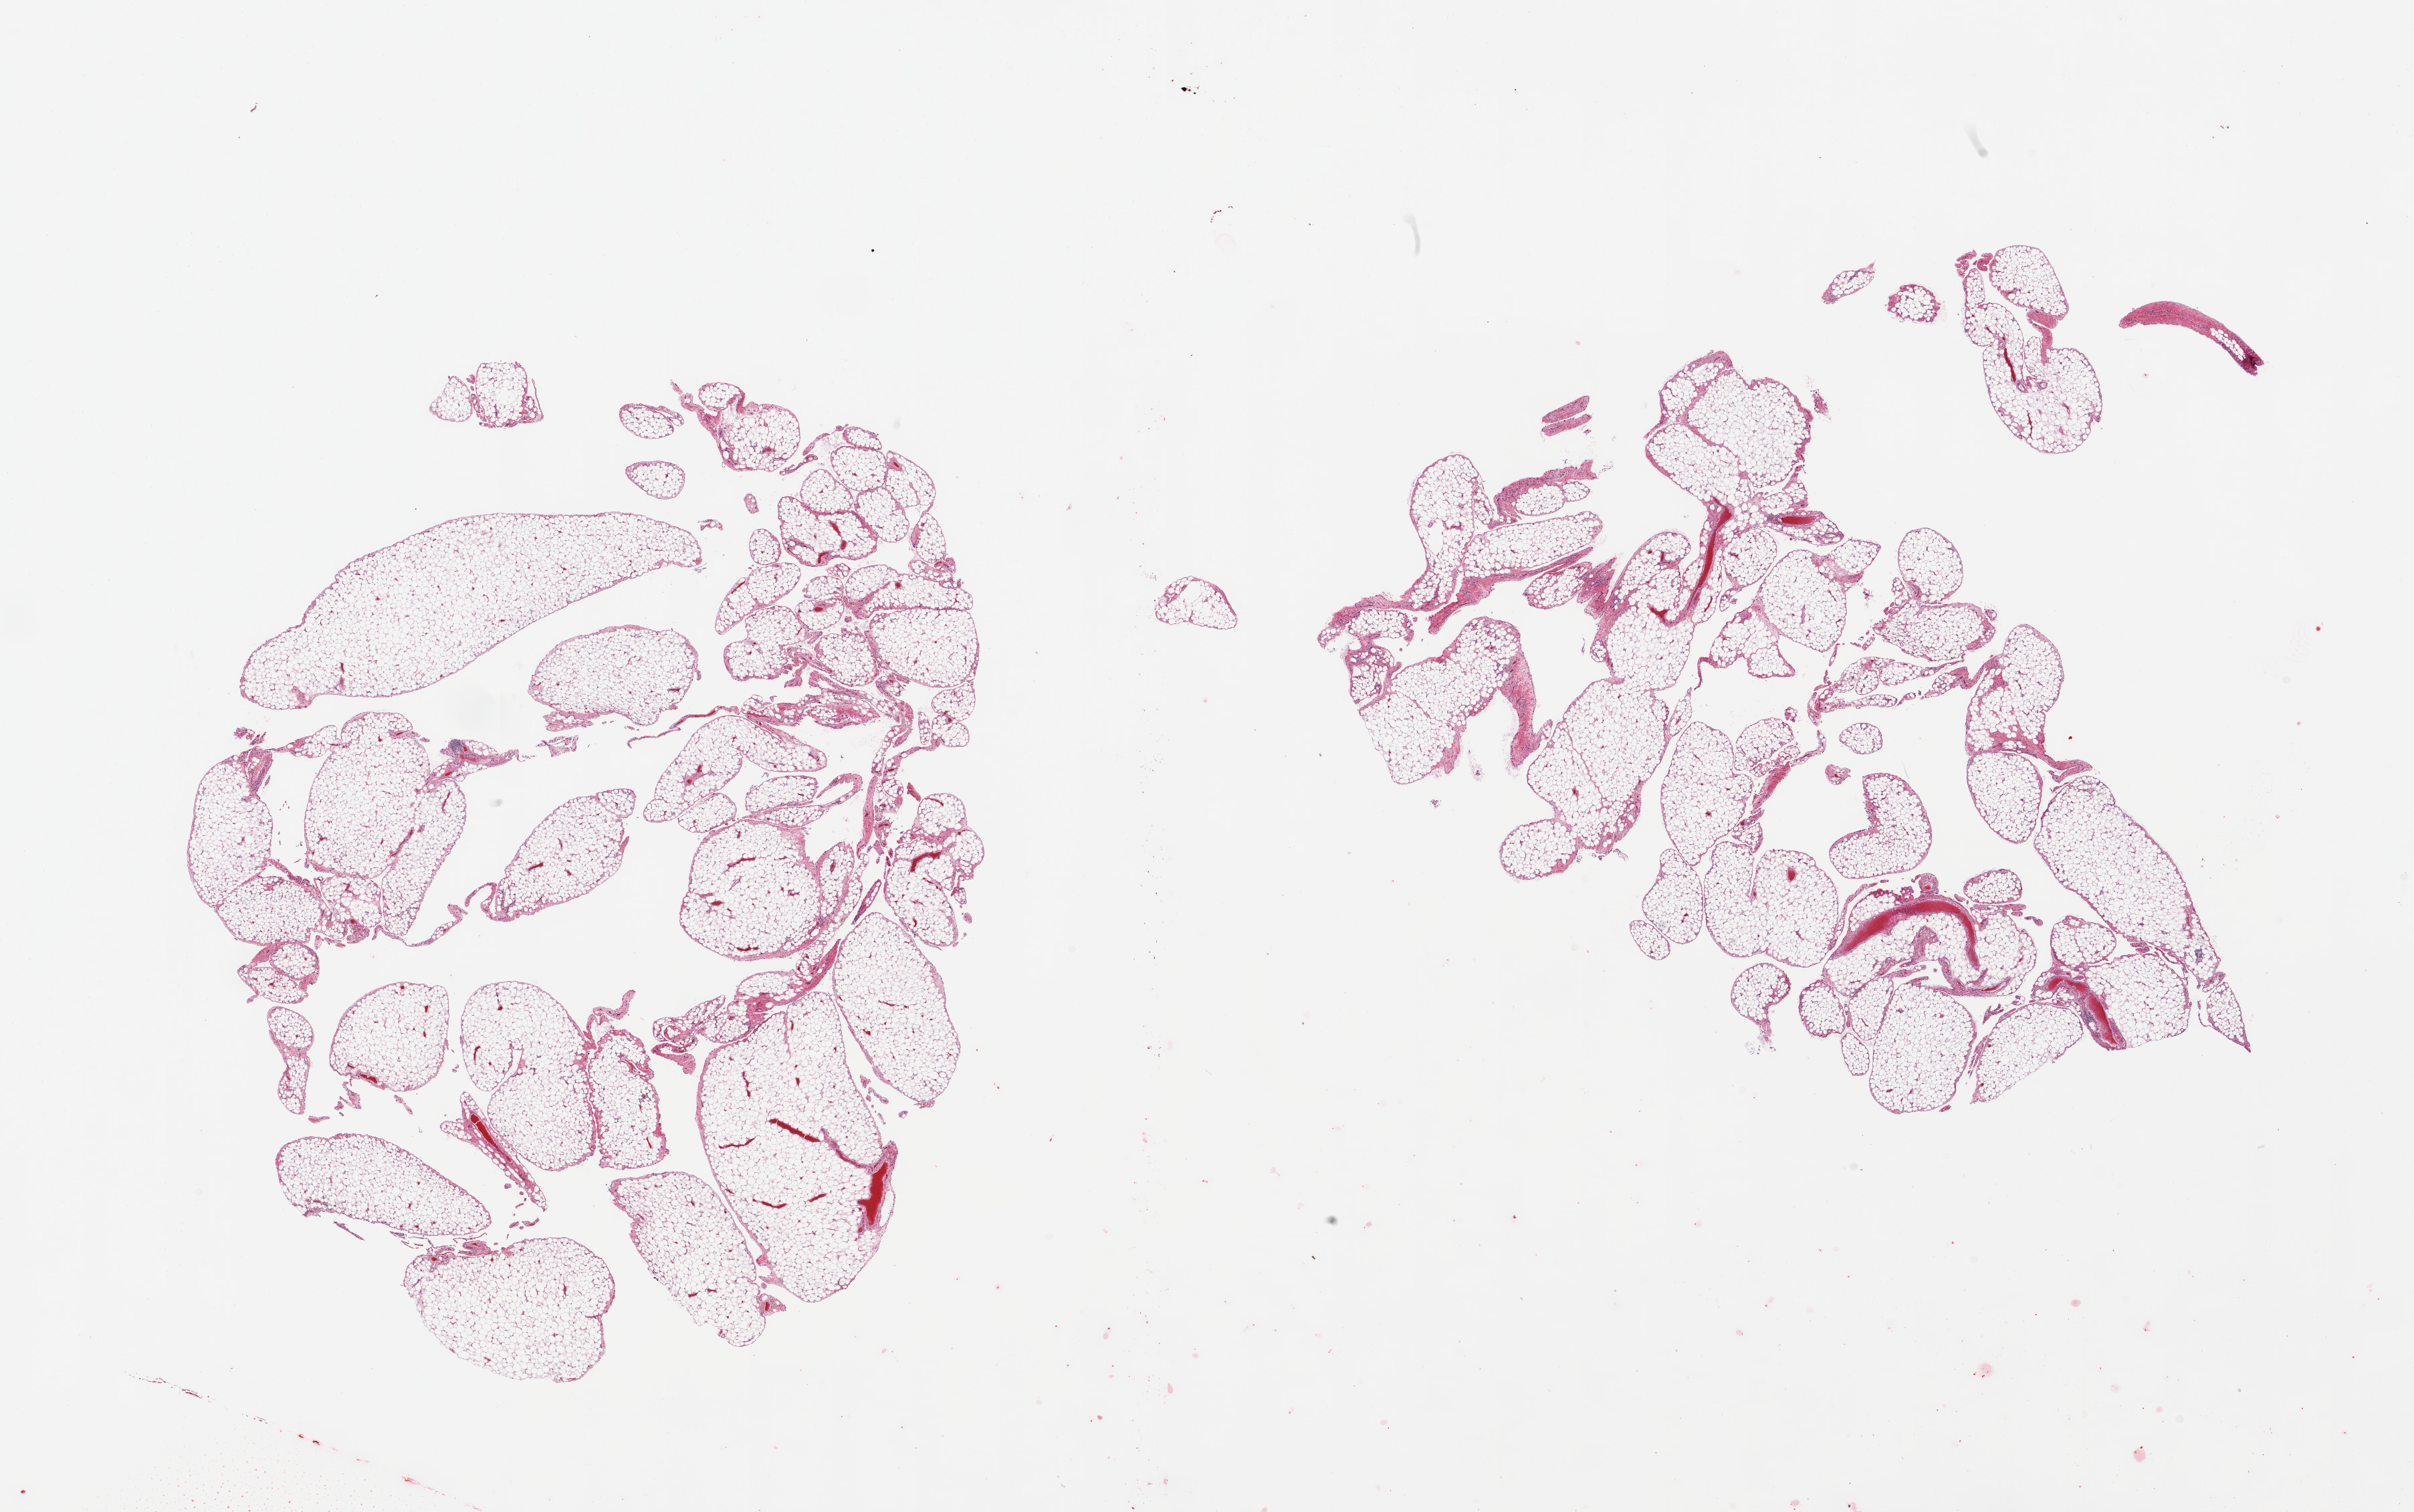
Whole-slide image, hematoxylin and eosin (H&E) stain, brightfield — a low-resolution overview of the entire scanned area, about 28.5 x 17.9 mm (slide scanned at 20x); PAXgene-fixed paraffin-embedded (PFPE) section; sampled site (target tissue): omentum; tissue donor sample. Donor sex: male.
Review note (as recorded): 2 fragmented pieces of lobulated mature adipose tissue.